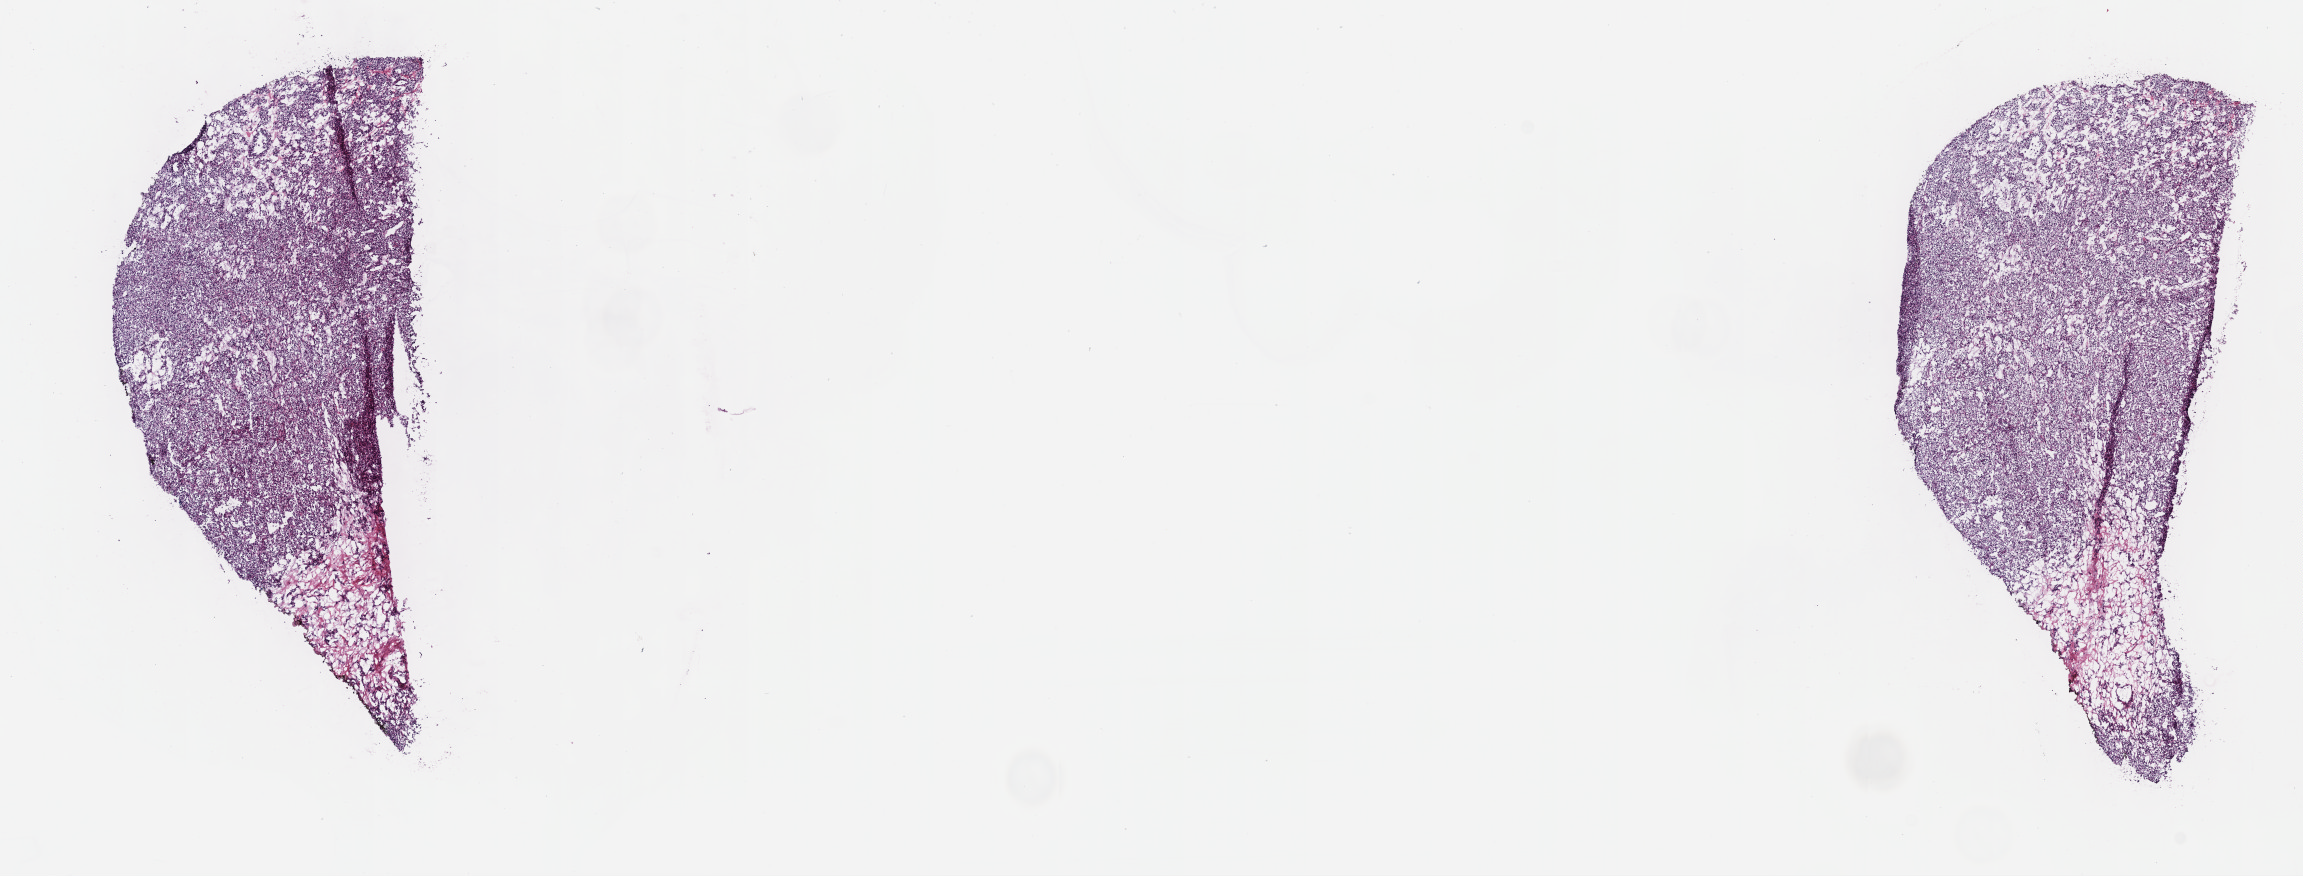
Digitized H&E-stained tissue section (whole slide), a low-resolution overview of the entire scanned area, about 18.6 x 7.1 mm (slide scanned at 40x), frozen section from the top of the tissue portion, primary tumour sample from the kidney. Patient: female, age at initial diagnosis 59 years. Histologic grade: G2 (moderately differentiated). Composition of this section per pathologist review: tumour cells 90%, tumour nuclei 95%, normal cells 0%, stromal cells 10%, necrosis 0%. Infiltration values recorded for this section: lymphocyte infiltration 0%, monocyte infiltration 0%, neutrophil infiltration 0%.
AJCC pathologic stage: I (7th edition). TNM: T1a NX MX. Histologic diagnosis: Clear cell adenocarcinoma, NOS. Laterality: left.